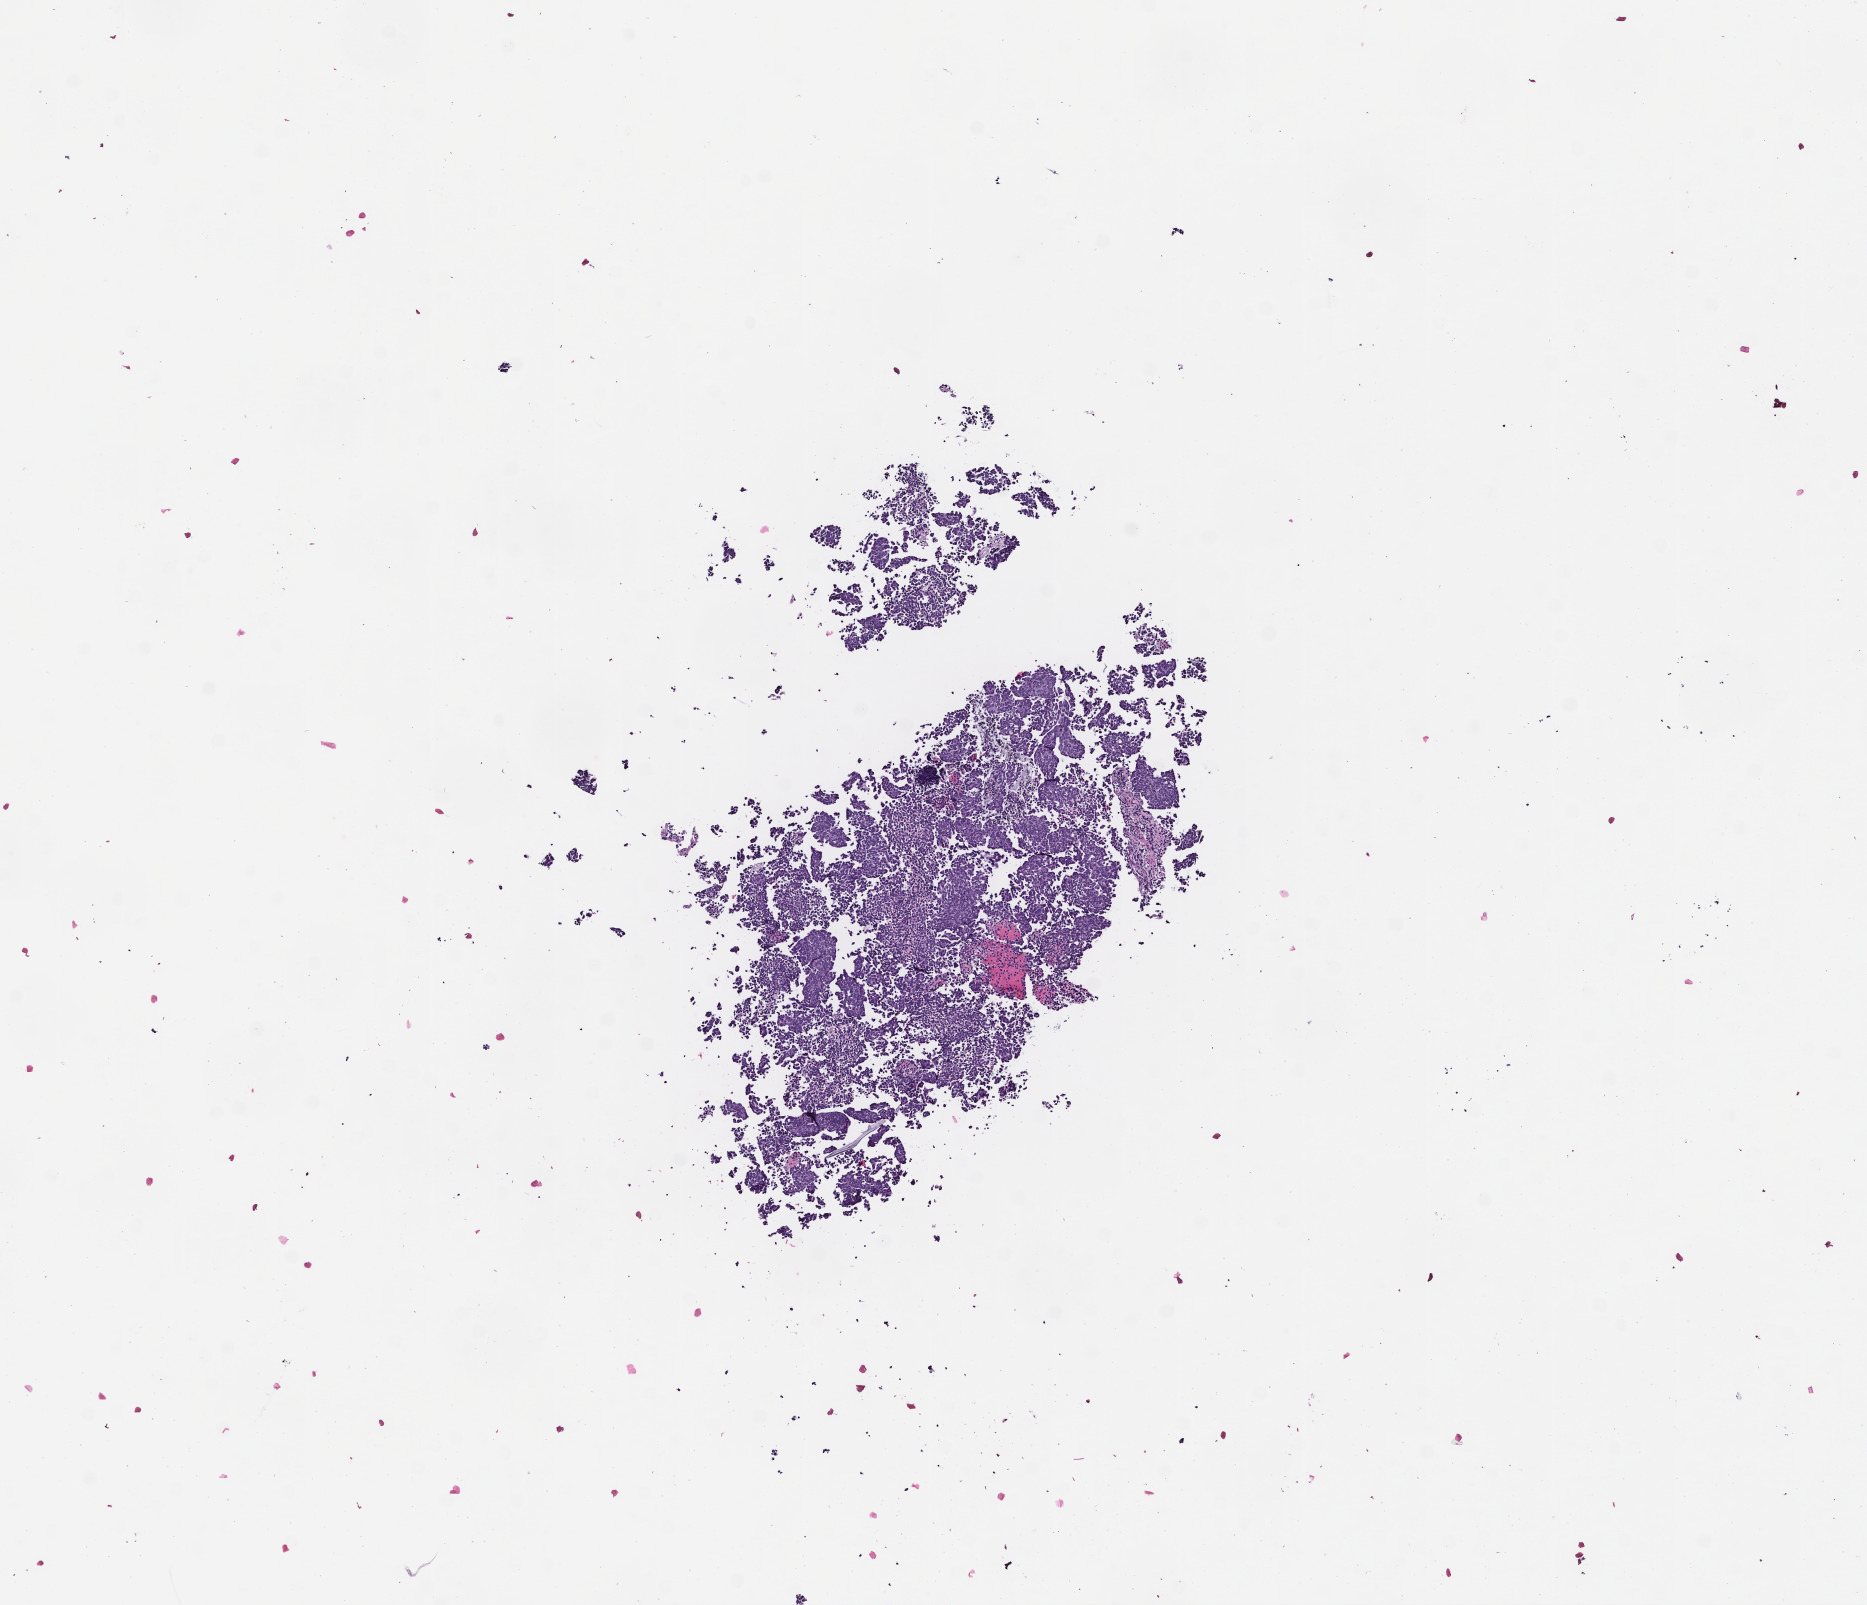
Haematoxylin and eosin whole-slide image, a low-resolution overview of the entire scanned area, about 7.5 x 6.5 mm, FFPE section, tissue site: lung. Male patient.
This section: primary tumor. Diagnosis: Small Cell Lung Carcinoma.